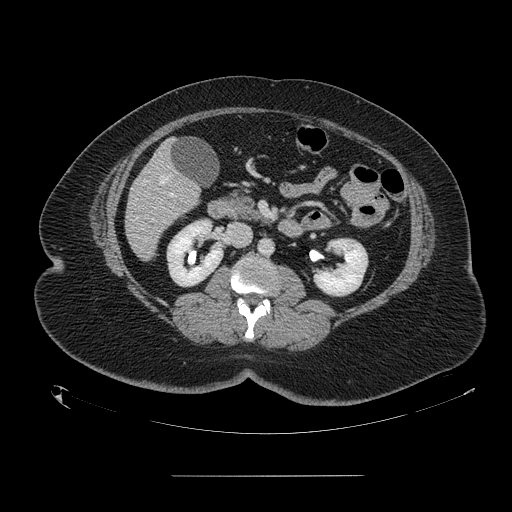
Contrast-enhanced abdominal CT, one axial slice. Slice 56 of 164 in the series (ordered by position). 120 kVp. Intravenous contrast given. Soft-tissue window (W 400 / L 40 HU). 2.5 mm slice thickness. 512 × 512 image matrix, field of view 495 × 495 mm. Female patient, age 52 years. Case-level facts recorded for this patient, not image findings: diagnosis: colorectal cancer liver metastases, imaged before liver resection; multiple liver metastases: yes; largest metastasis: 3.5 cm.
Outlined on this slice (outlined manually by an expert reader):
- hepatic veins: bounding box [x1, y1, x2, y2] px = [136, 176, 169, 219]
- liver: [126, 144, 201, 260]
- portal vein (with intrahepatic branches): [169, 193, 173, 196]